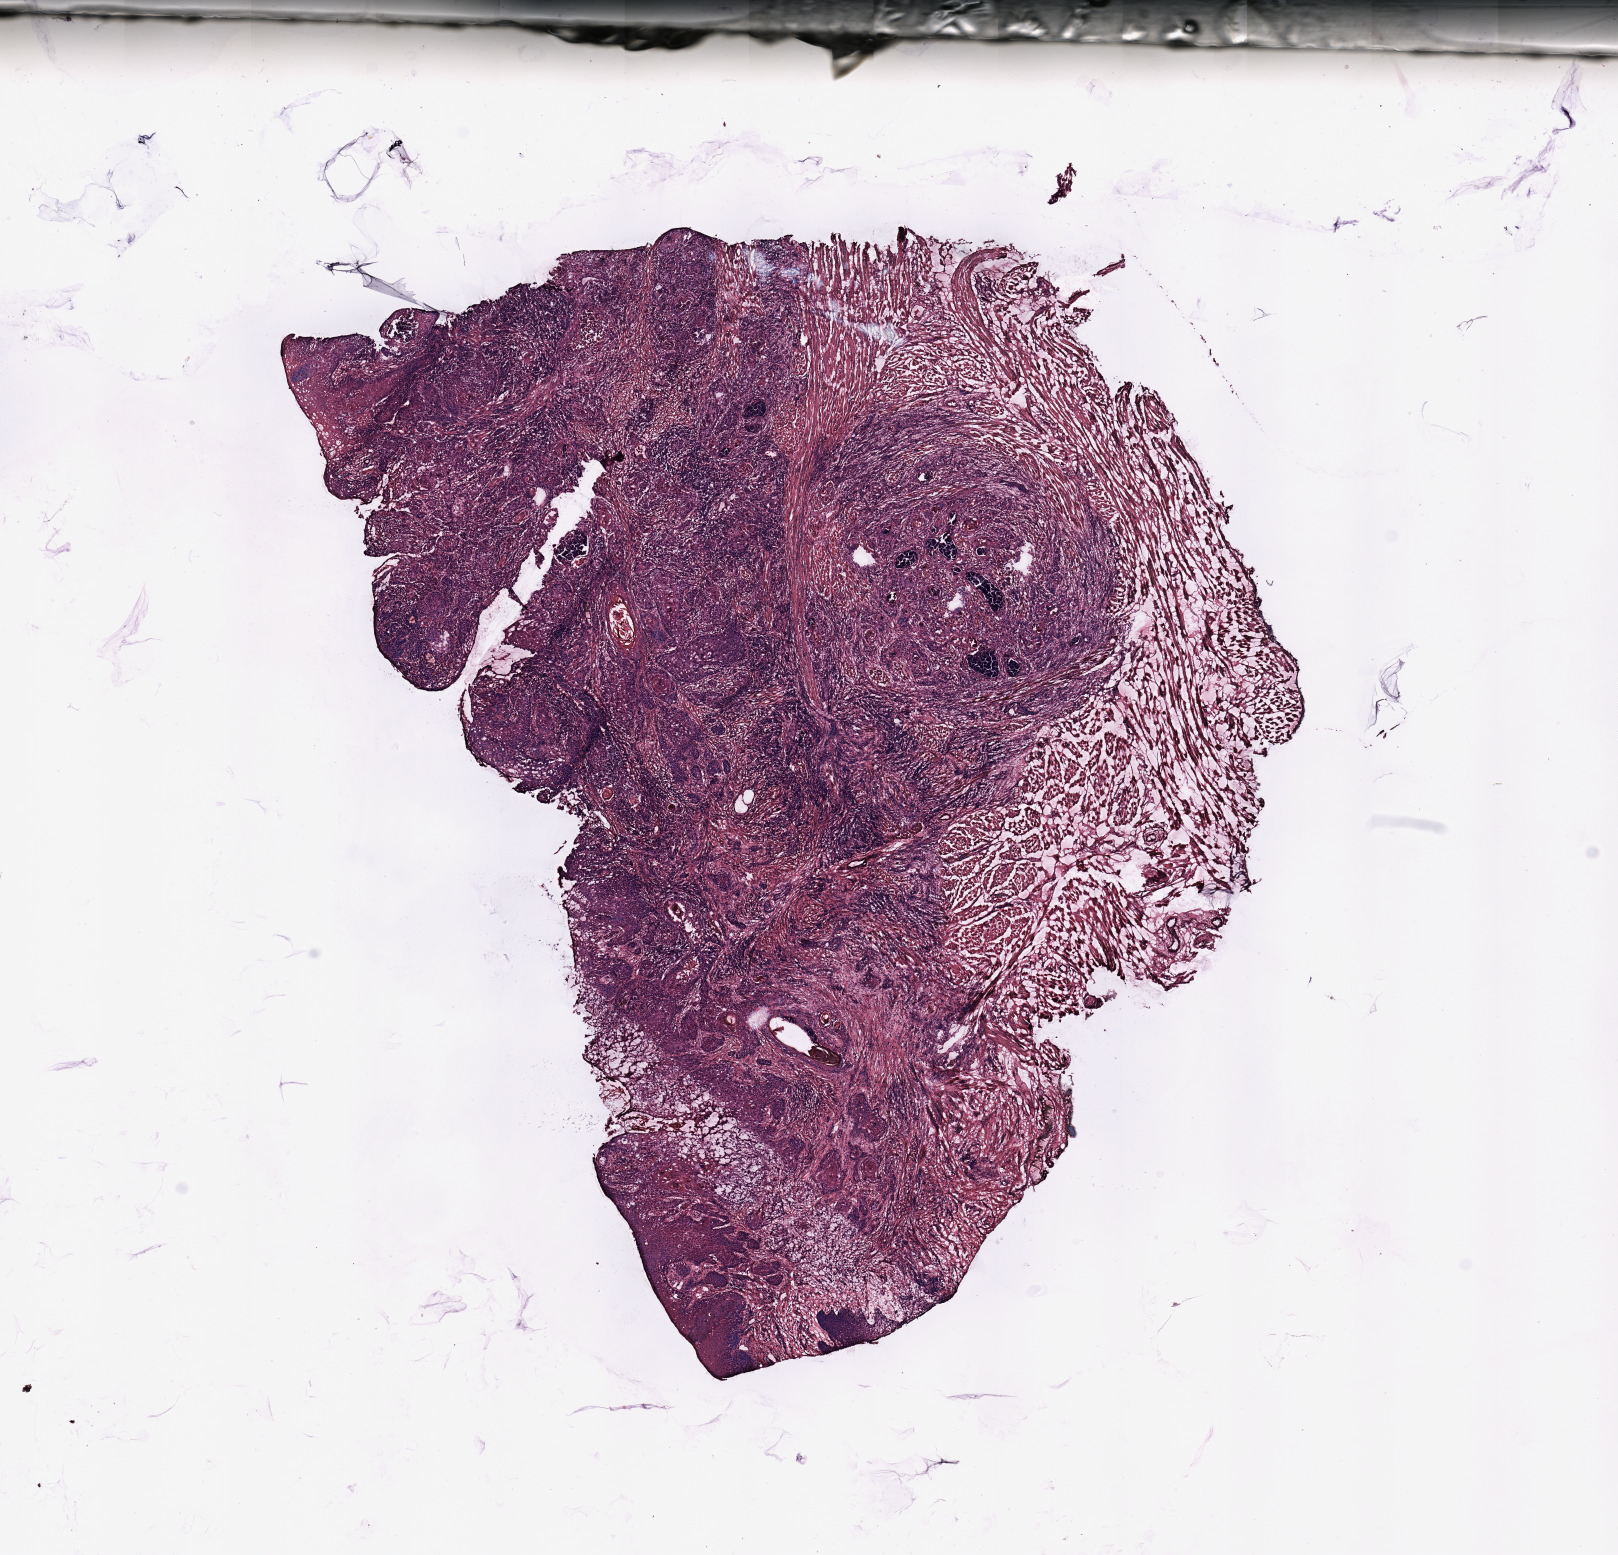
Digitized Hematoxylin and eosin (H&E) stained tissue section (whole slide) — shown as a low-resolution overview of the whole scanned area (about 12.8 x 12.3 mm), tumour tissue sample, sampled site: tongue. Patient: male, age 67 years. Composition of this section per pathologist review: tumour nuclei 80%, necrosis 7%.
Diagnosis: Squamous cell carcinoma, NOS (tongue, NOS).